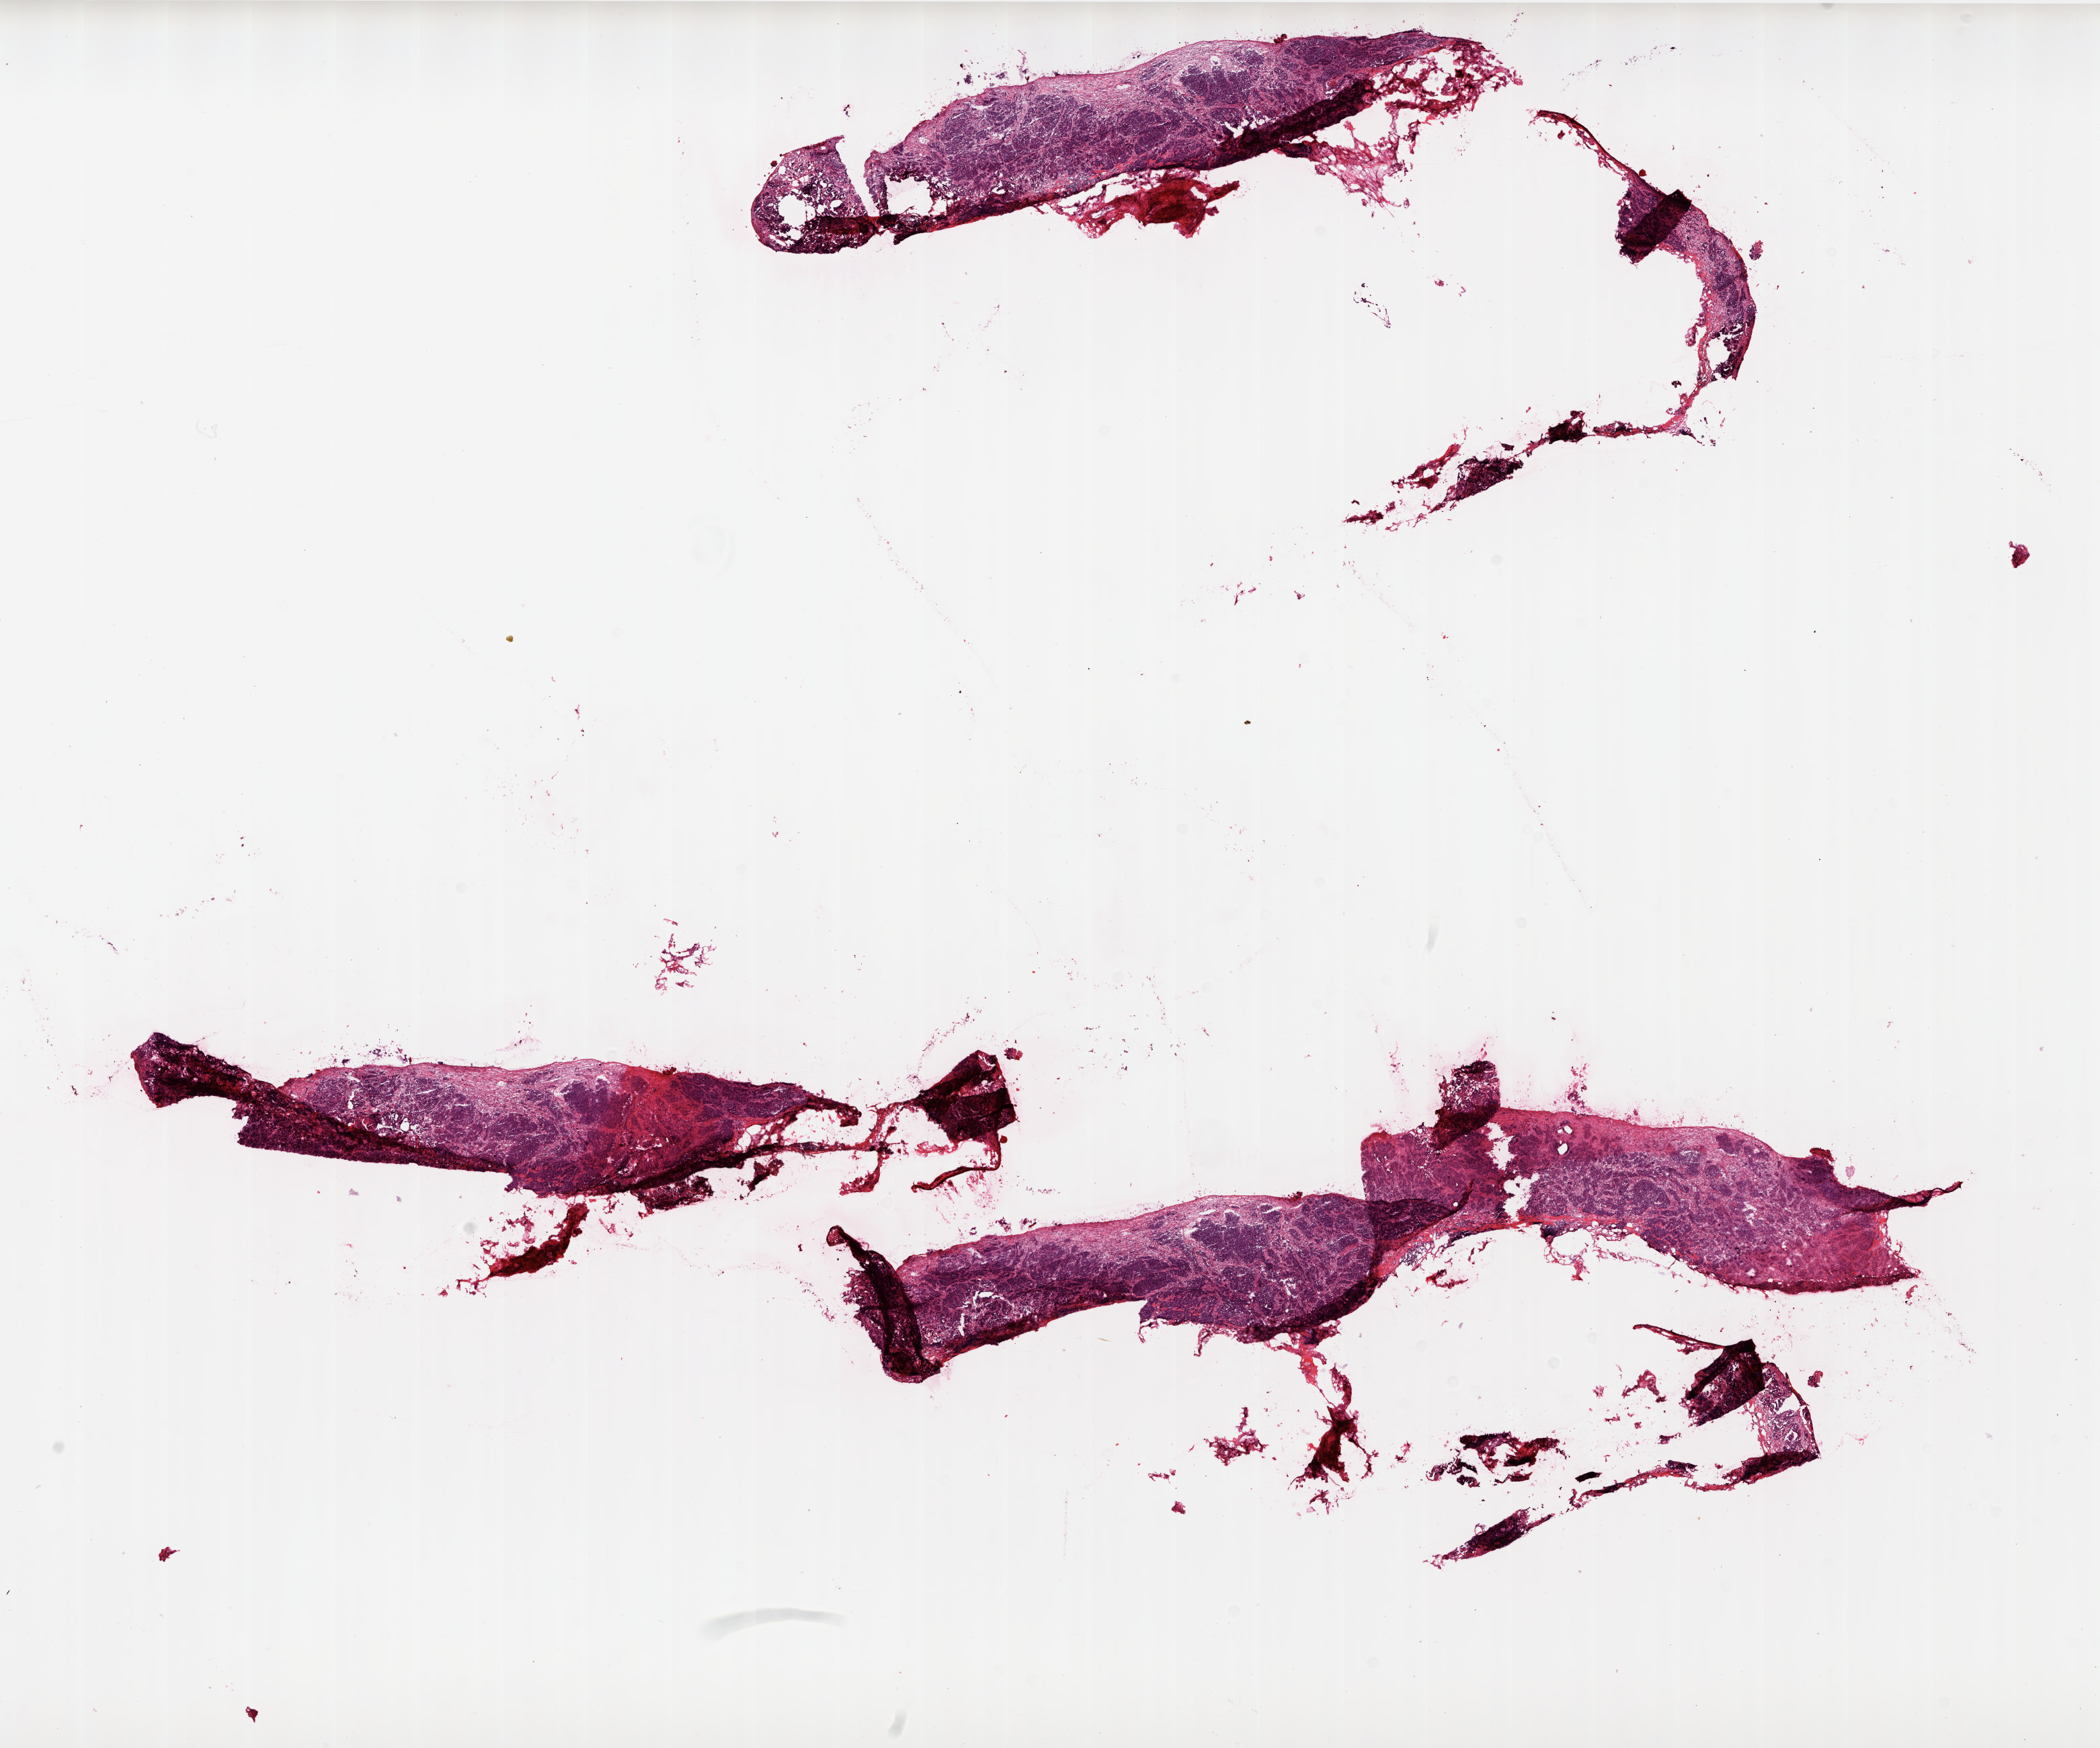
Hematoxylin and eosin (H&E) stained whole-slide image — a low-resolution overview of the entire scanned area, about 25.0 x 20.8 mm, frozen section from the top of the tissue portion, sample: primary tumour, ovary. Patient: female, age at initial diagnosis 72 years. Histologic grade: G3 (poorly differentiated). Pathologist review of this section (percent, as recorded): tumour cells 95%, tumour nuclei 93%, normal cells 0%, stromal cells 4%, necrosis 1%.
* diagnosis: Serous cystadenocarcinoma, NOS
* FIGO stage: IV
* laterality: bilateral